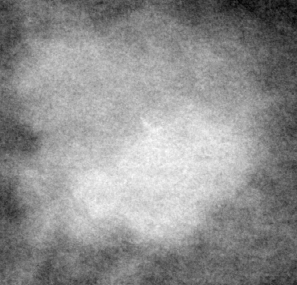
Crop from a digitized film mammogram around one marked abnormality; right breast; CC view; BI-RADS breast density category 2 (scale 1–4).
Finding: mass, shape lobulated, margins circumscribed / ill defined; BI-RADS assessment category 4; subtlety rating 4 on a 1 (subtle) to 5 (obvious) scale; pathology result (as recorded, not read from the image): malignant.